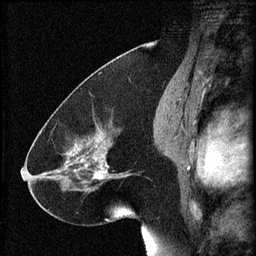
Breast MRI (dynamic contrast-enhanced), one sagittal slice; slice 35 of 60 in the series (ordered by position); 3 images stored at this slice position (order not interpretable as contrast timing); 1.5 T; TE 4.2 ms, TR 8.2 ms; 2 mm slice thickness; 256 × 256 image matrix, field of view 180 × 180 mm. Patient: female, 41 years.
Structures marked on this image (semi-automatic segmentation, software-assisted and operator-edited):
- analysis volume of interest (the breast-tissue region the enhancement analysis was run in; not a lesion): bounding box [x1, y1, x2, y2] px = [72, 120, 134, 195]
- tumour enhancement mask (voxels above the 70 % enhancement threshold inside the analysis volume of interest): [72, 128, 129, 179]